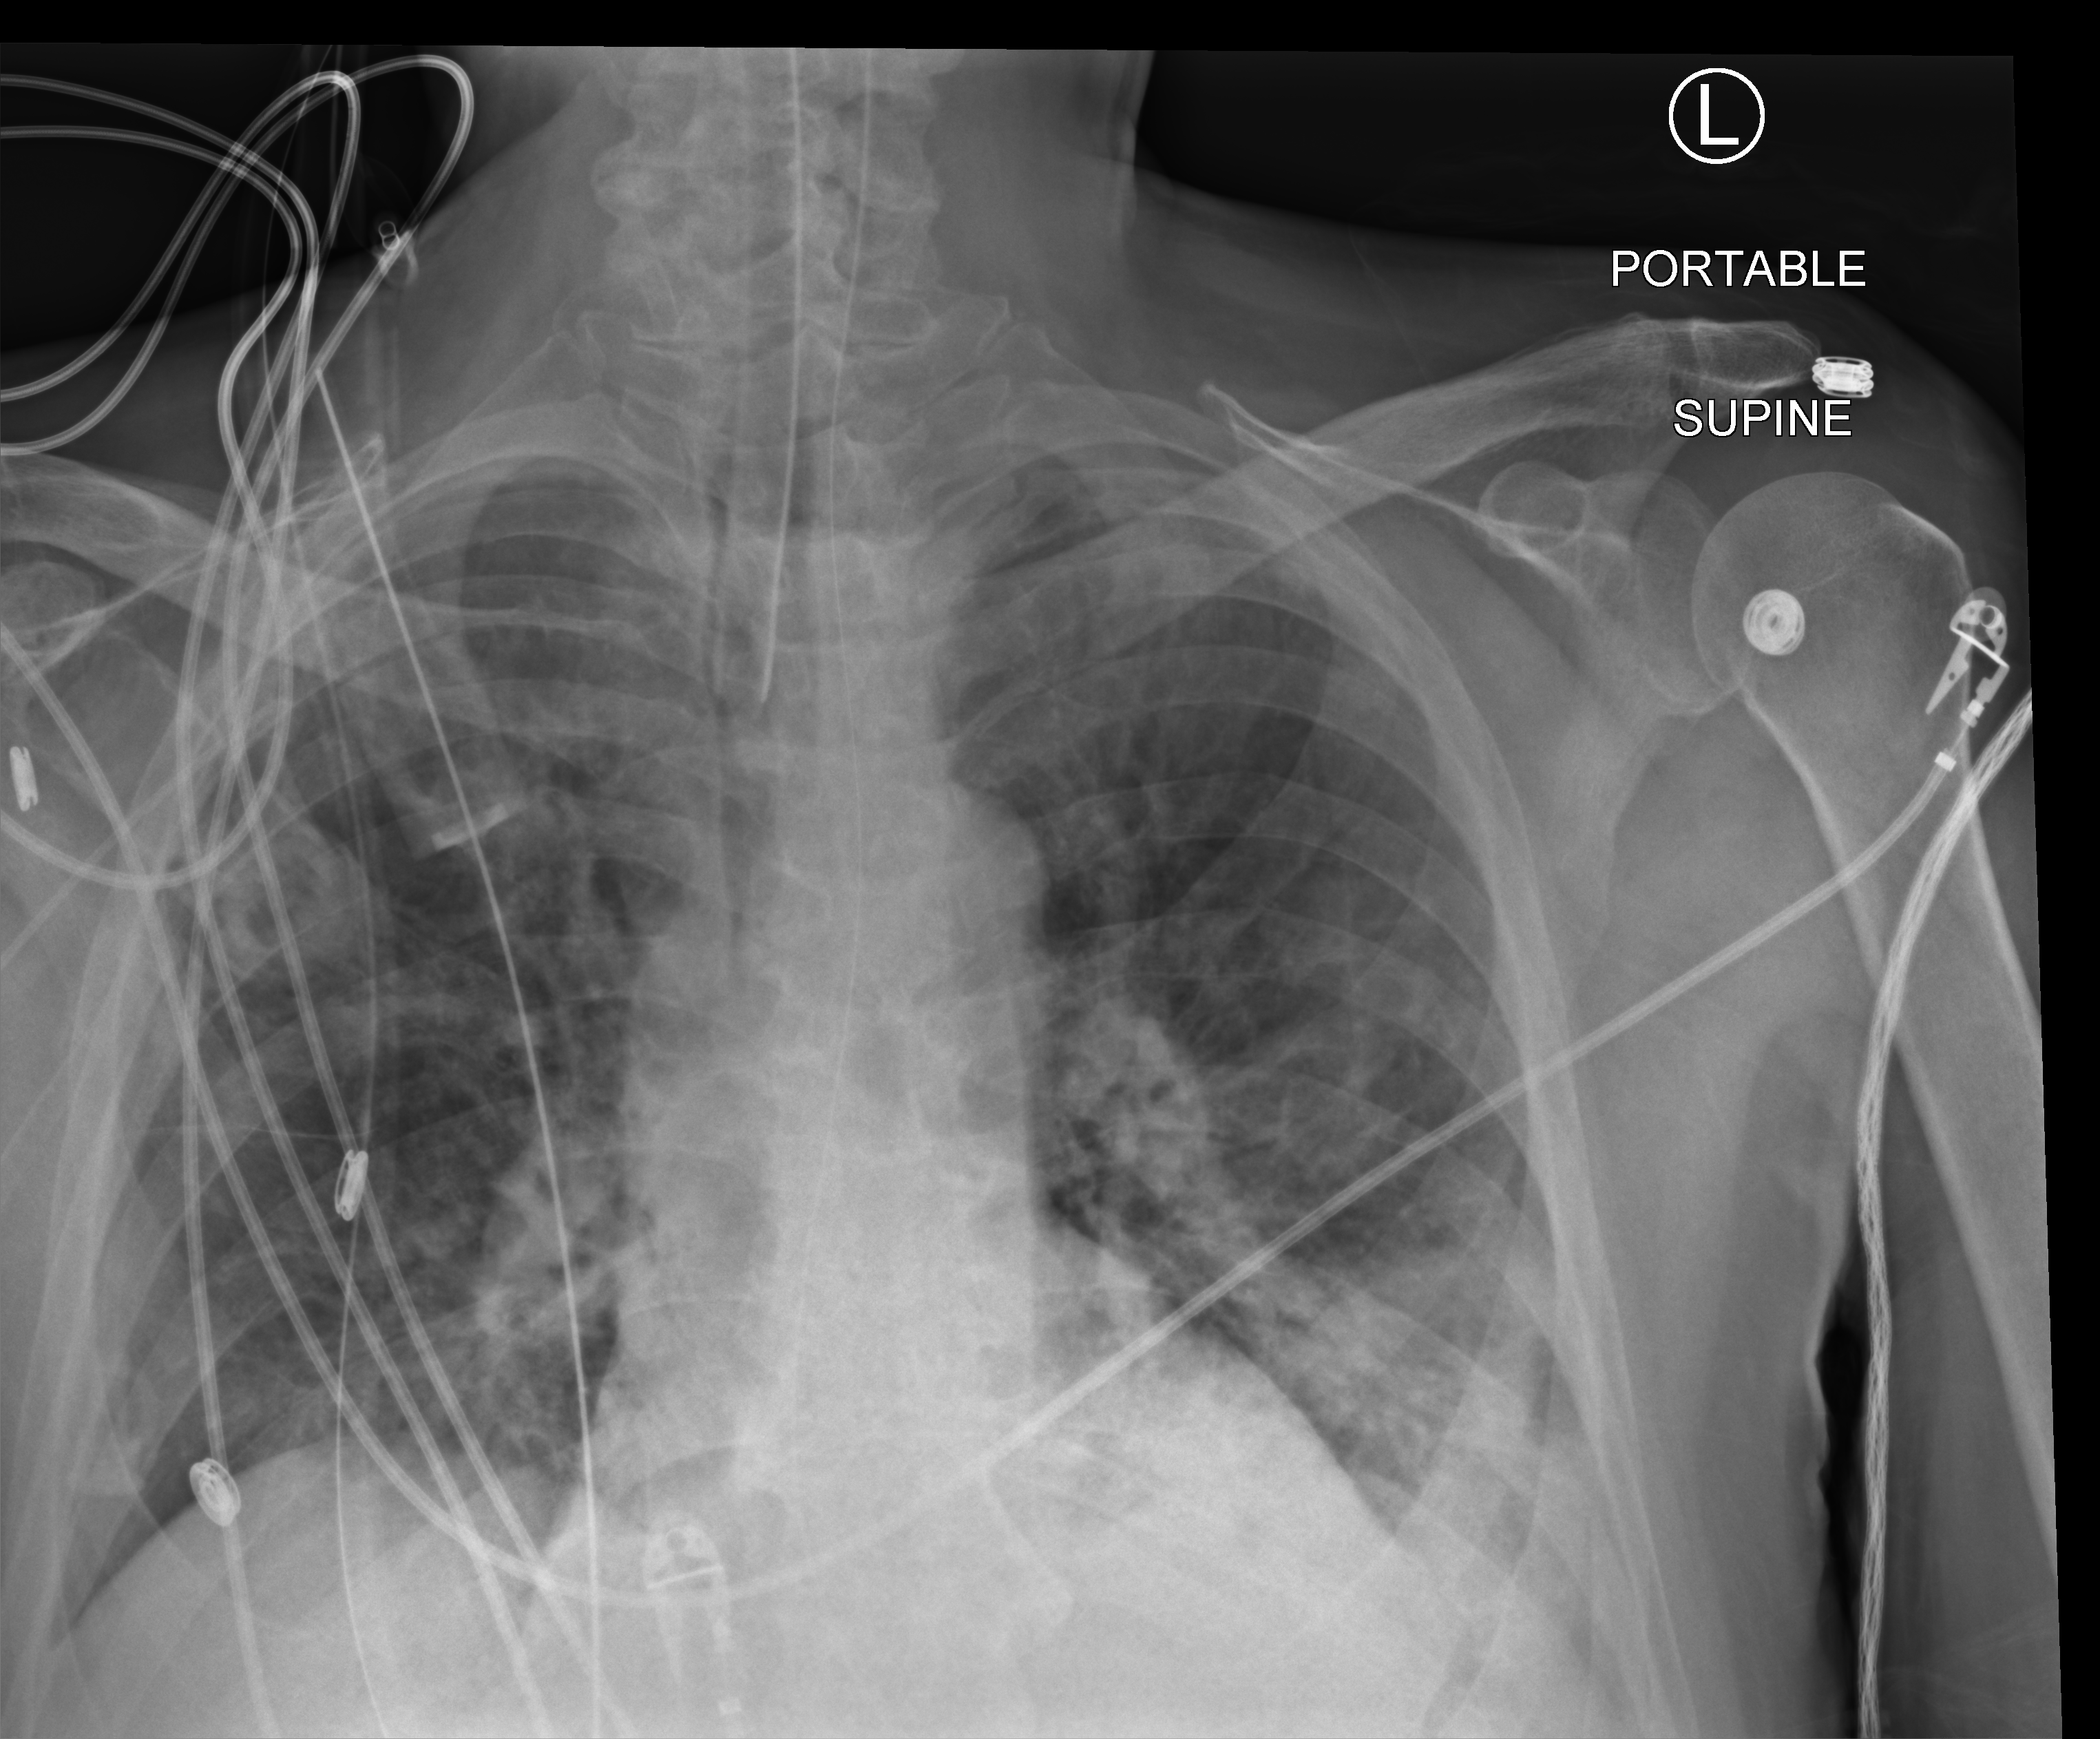
Chest X-ray (portable). Patient hospitalised with COVID-19; male, aged 60–74 years.
Hospital-stay facts (about this admission, not read from this image; timing relative to this image not recorded): smoking status (admission record): never; hypertension (admission record): yes.